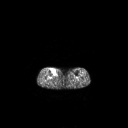
FDG PET of an extremity soft-tissue mass (from a PET/CT study), one axial slice. Position 139 of 267 along the scan axis. 3.27 mm slice thickness. 128 × 128 image matrix, field of view 700 × 700 mm. Patient: female, 65 years. Case-level facts recorded for this patient, not image findings: histological type: undifferentiated – high grade; grade: high; site of the primary tumour: right thigh.
Annotated regions visible in this slice (expert contour drawn on MRI and transferred to this co-registered scan by the dataset authors):
- gross tumour volume (mass): box from (x=51, y=68) to (x=56, y=75) px